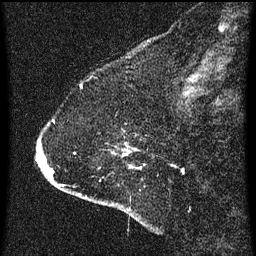
Breast MRI (dynamic contrast-enhanced), one sagittal slice; dynamic contrast-enhanced series, image 2 of 3 at this slice position (ordered by acquisition); 1.5 T; TE 4.2 ms, TR 8 ms; 2 mm slice thickness; 256 × 256 image matrix, field of view 180 × 180 mm. Female patient, age 47 years.
Annotated regions visible in this slice (semi-automatically segmented with operator editing):
- analysis volume of interest (the breast-tissue region the enhancement analysis was run in; not a lesion): box from (x=36, y=120) to (x=146, y=213) px
- tumour enhancement mask (voxels above the 70 % enhancement threshold inside the analysis volume of interest): (x=50, y=166)–(x=132, y=171)